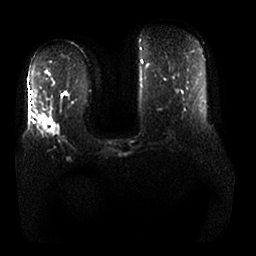
Breast MRI, one axial slice. Position 12 of 25 along the scan axis. Diffusion-weighted series; image 2 of 4 stored at this slice position (different b-values; order by instance number). 1.5 T. 4 mm slice thickness. 256 × 256 image matrix, field of view 380 × 380 mm. Female patient.
Annotated regions visible in this slice (outlined manually by an expert reader):
- tumour on diffusion-weighted imaging: bounding box (x1, y1, x2, y2) in pixels: (39, 122, 60, 136)